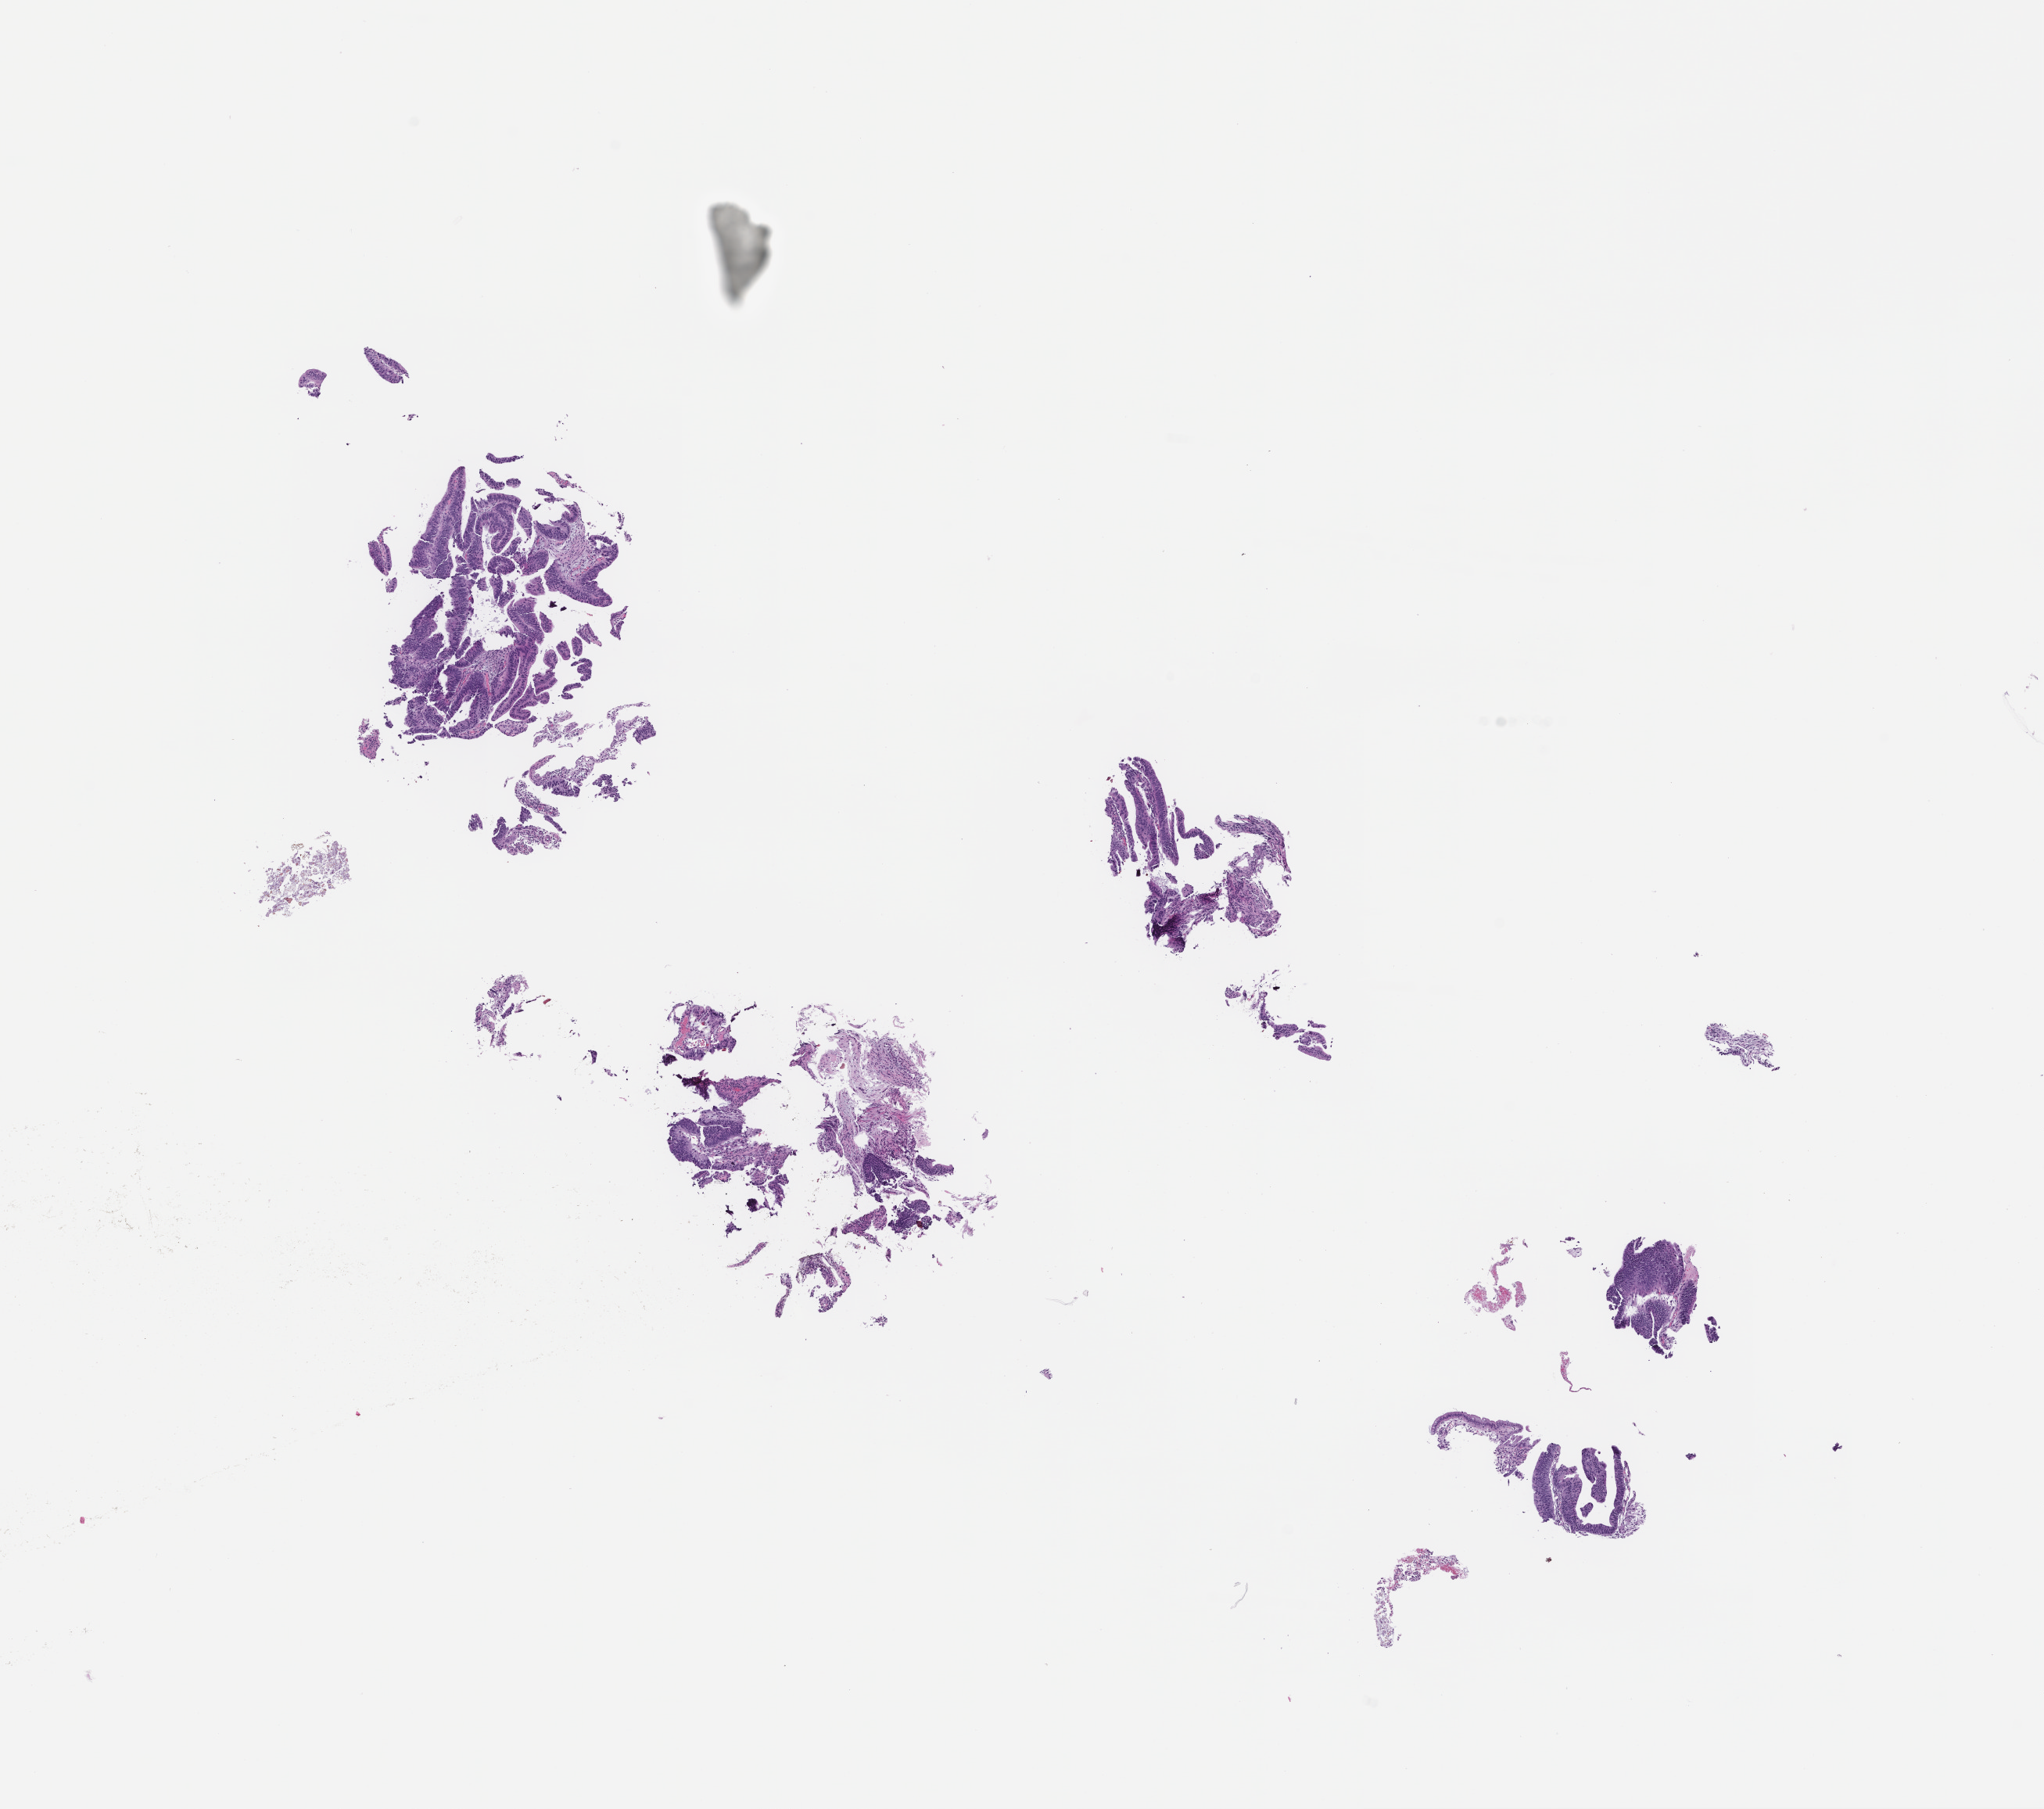
Whole-slide image, hematoxylin and eosin (H&E) stain, a low-resolution overview of the entire scanned area, about 10.6 x 9.3 mm; FFPE section; site: colon; specimen time point: archival tissue. Male patient.
This section: primary tumor. Diagnosis: Colorectal Carcinoma.